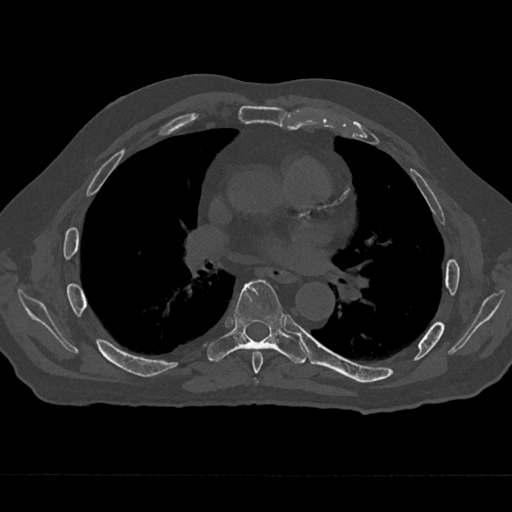
CT including the spine, one axial slice. Slice 386 of 797 in the series (ordered by position). Reconstruction kernel Br40s/3. 120 kVp. Bone window (W 1800 / L 400 HU). 0.5 mm slice thickness. 512 × 512 image matrix, field of view 377 × 377 mm. Male patient, age 75 years. Case-level facts recorded for this patient, not image findings: primary cancer: renal.
Structures marked on this image (semi-automatic segmentation, software-assisted and operator-edited):
- T6 vertebra: bounding box <252,351,263,383> (left, top, right, bottom; pixels)
- T7 vertebra: <207,280,306,364>